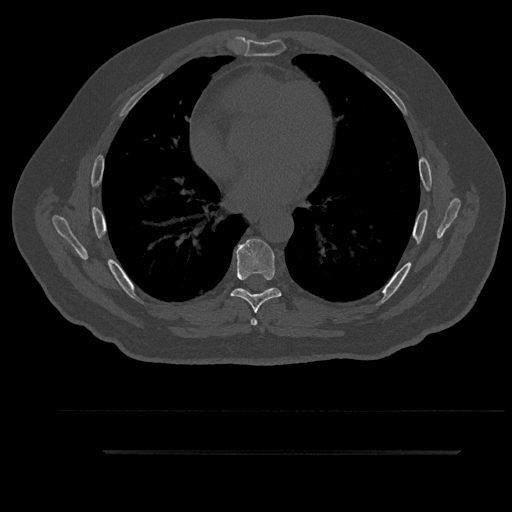
CT including the spine, one axial slice. Position 525 of 797 along the scan axis. Reconstruction kernel Br40s/3. Bone window (W 1800 / L 400 HU). 0.5 mm slice thickness. 512 × 512 image matrix, field of view 432 × 432 mm. Male patient, age 63 years. From the clinical record (not read from this slice): primary cancer: renal; vertebrae with lytic lesions (as recorded): T8.
Annotated regions visible in this slice (semi-automatically segmented with operator editing):
- T6 vertebra: box from (x=251, y=289) to (x=269, y=326) px
- T7 vertebra: (x=231, y=239)–(x=281, y=313)